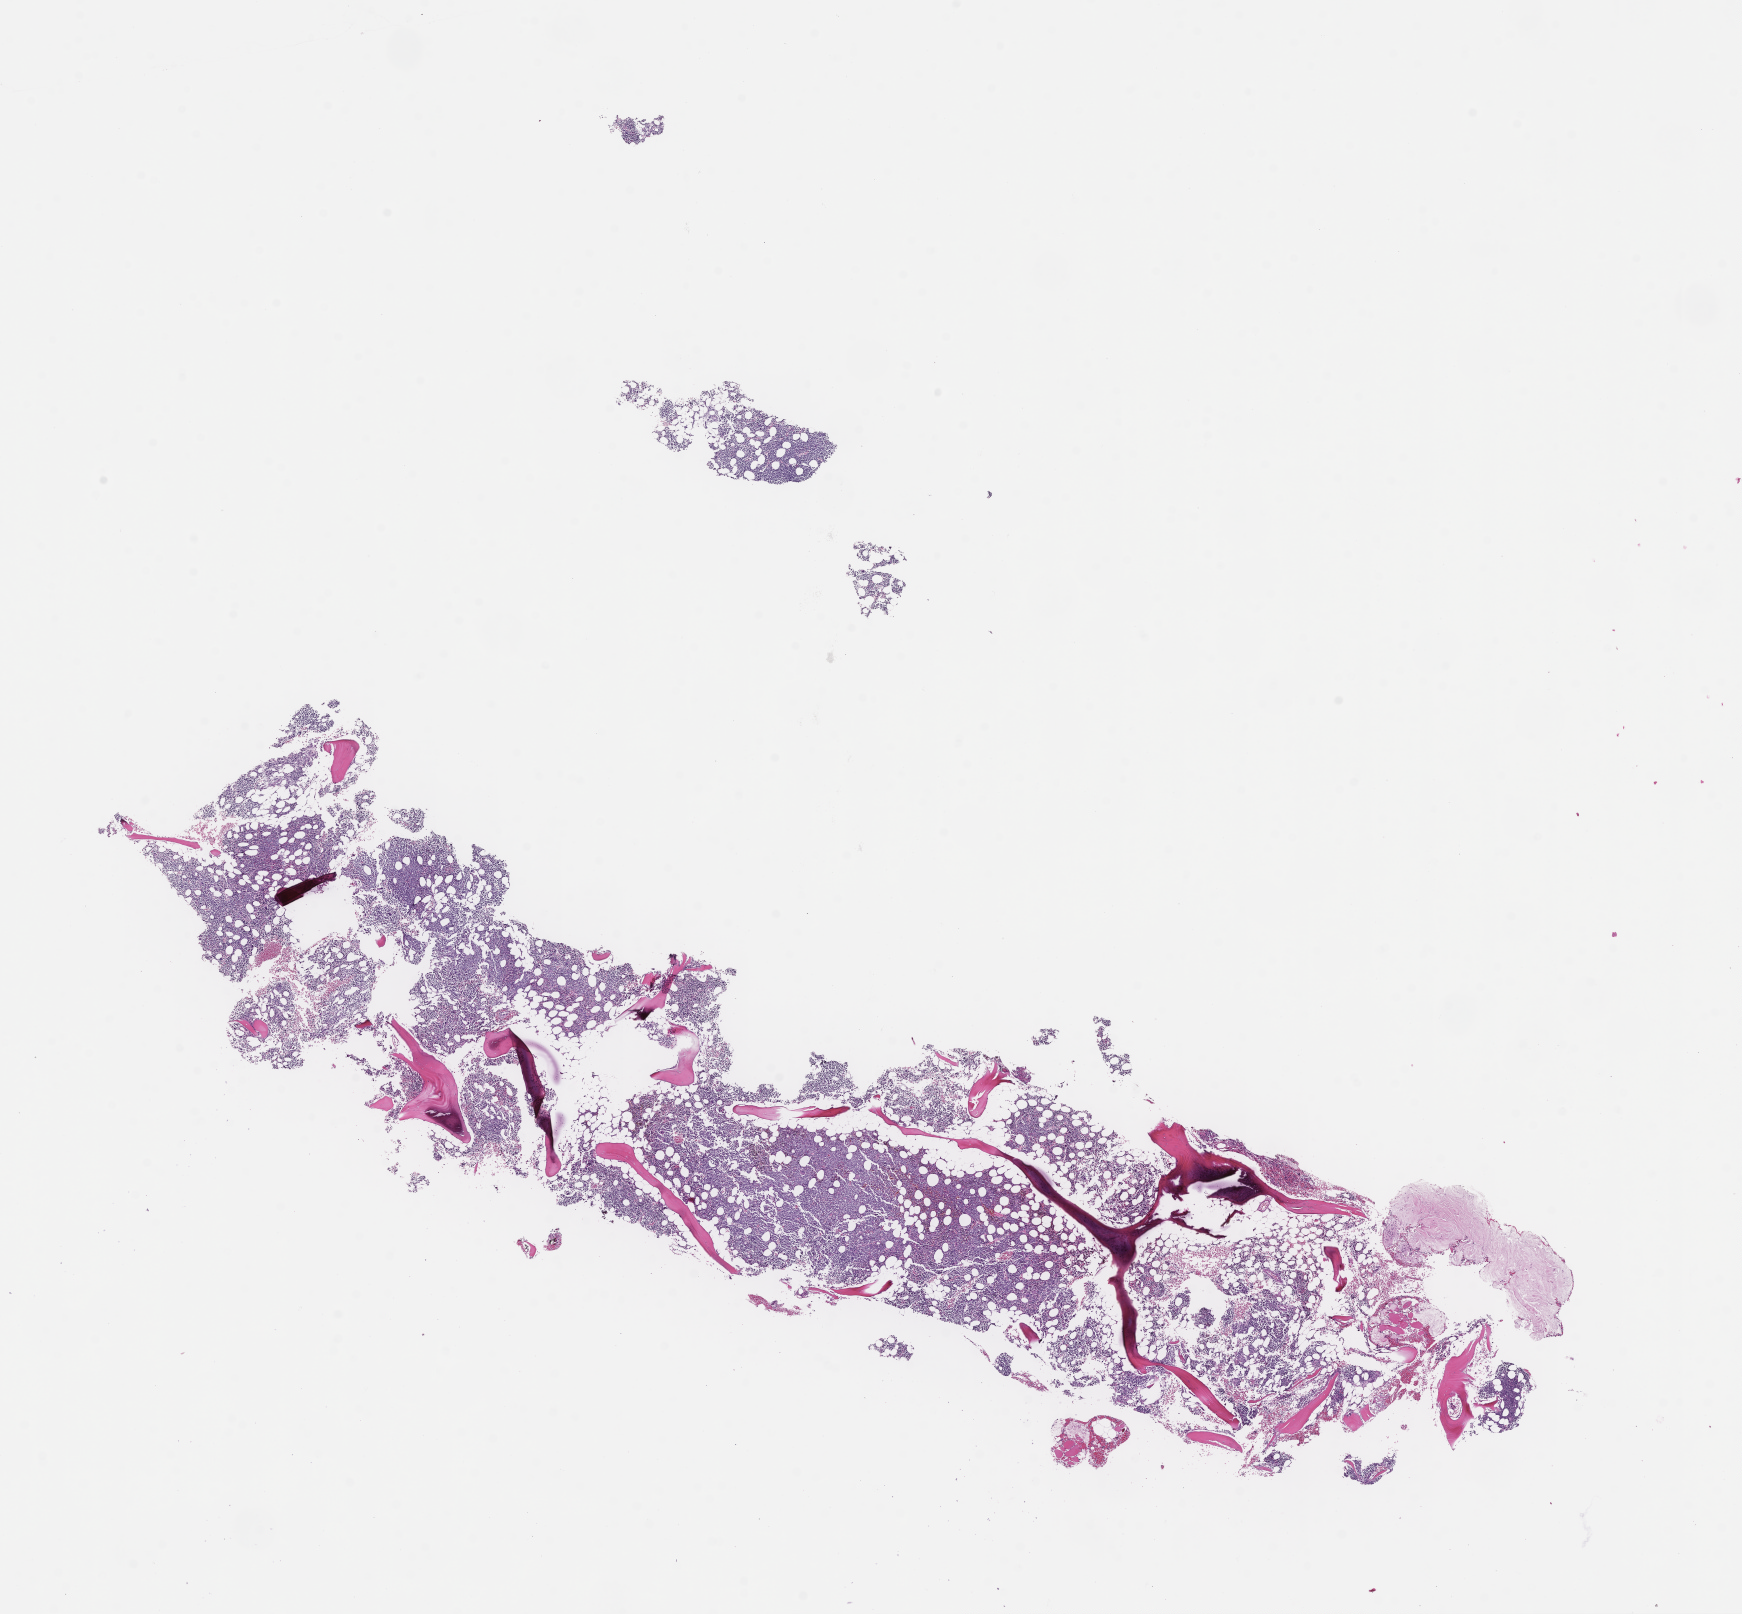
Digitized haematoxylin and eosin-stained section — a low-resolution overview of the entire scanned area, about 14.1 x 13.0 mm; formalin-fixed, paraffin-embedded (FFPE) tissue; site: bone marrow; specimen time point: archival tissue. Patient sex: female.
• this section: primary tumour tissue
• diagnosis: Plasma Cell Myeloma